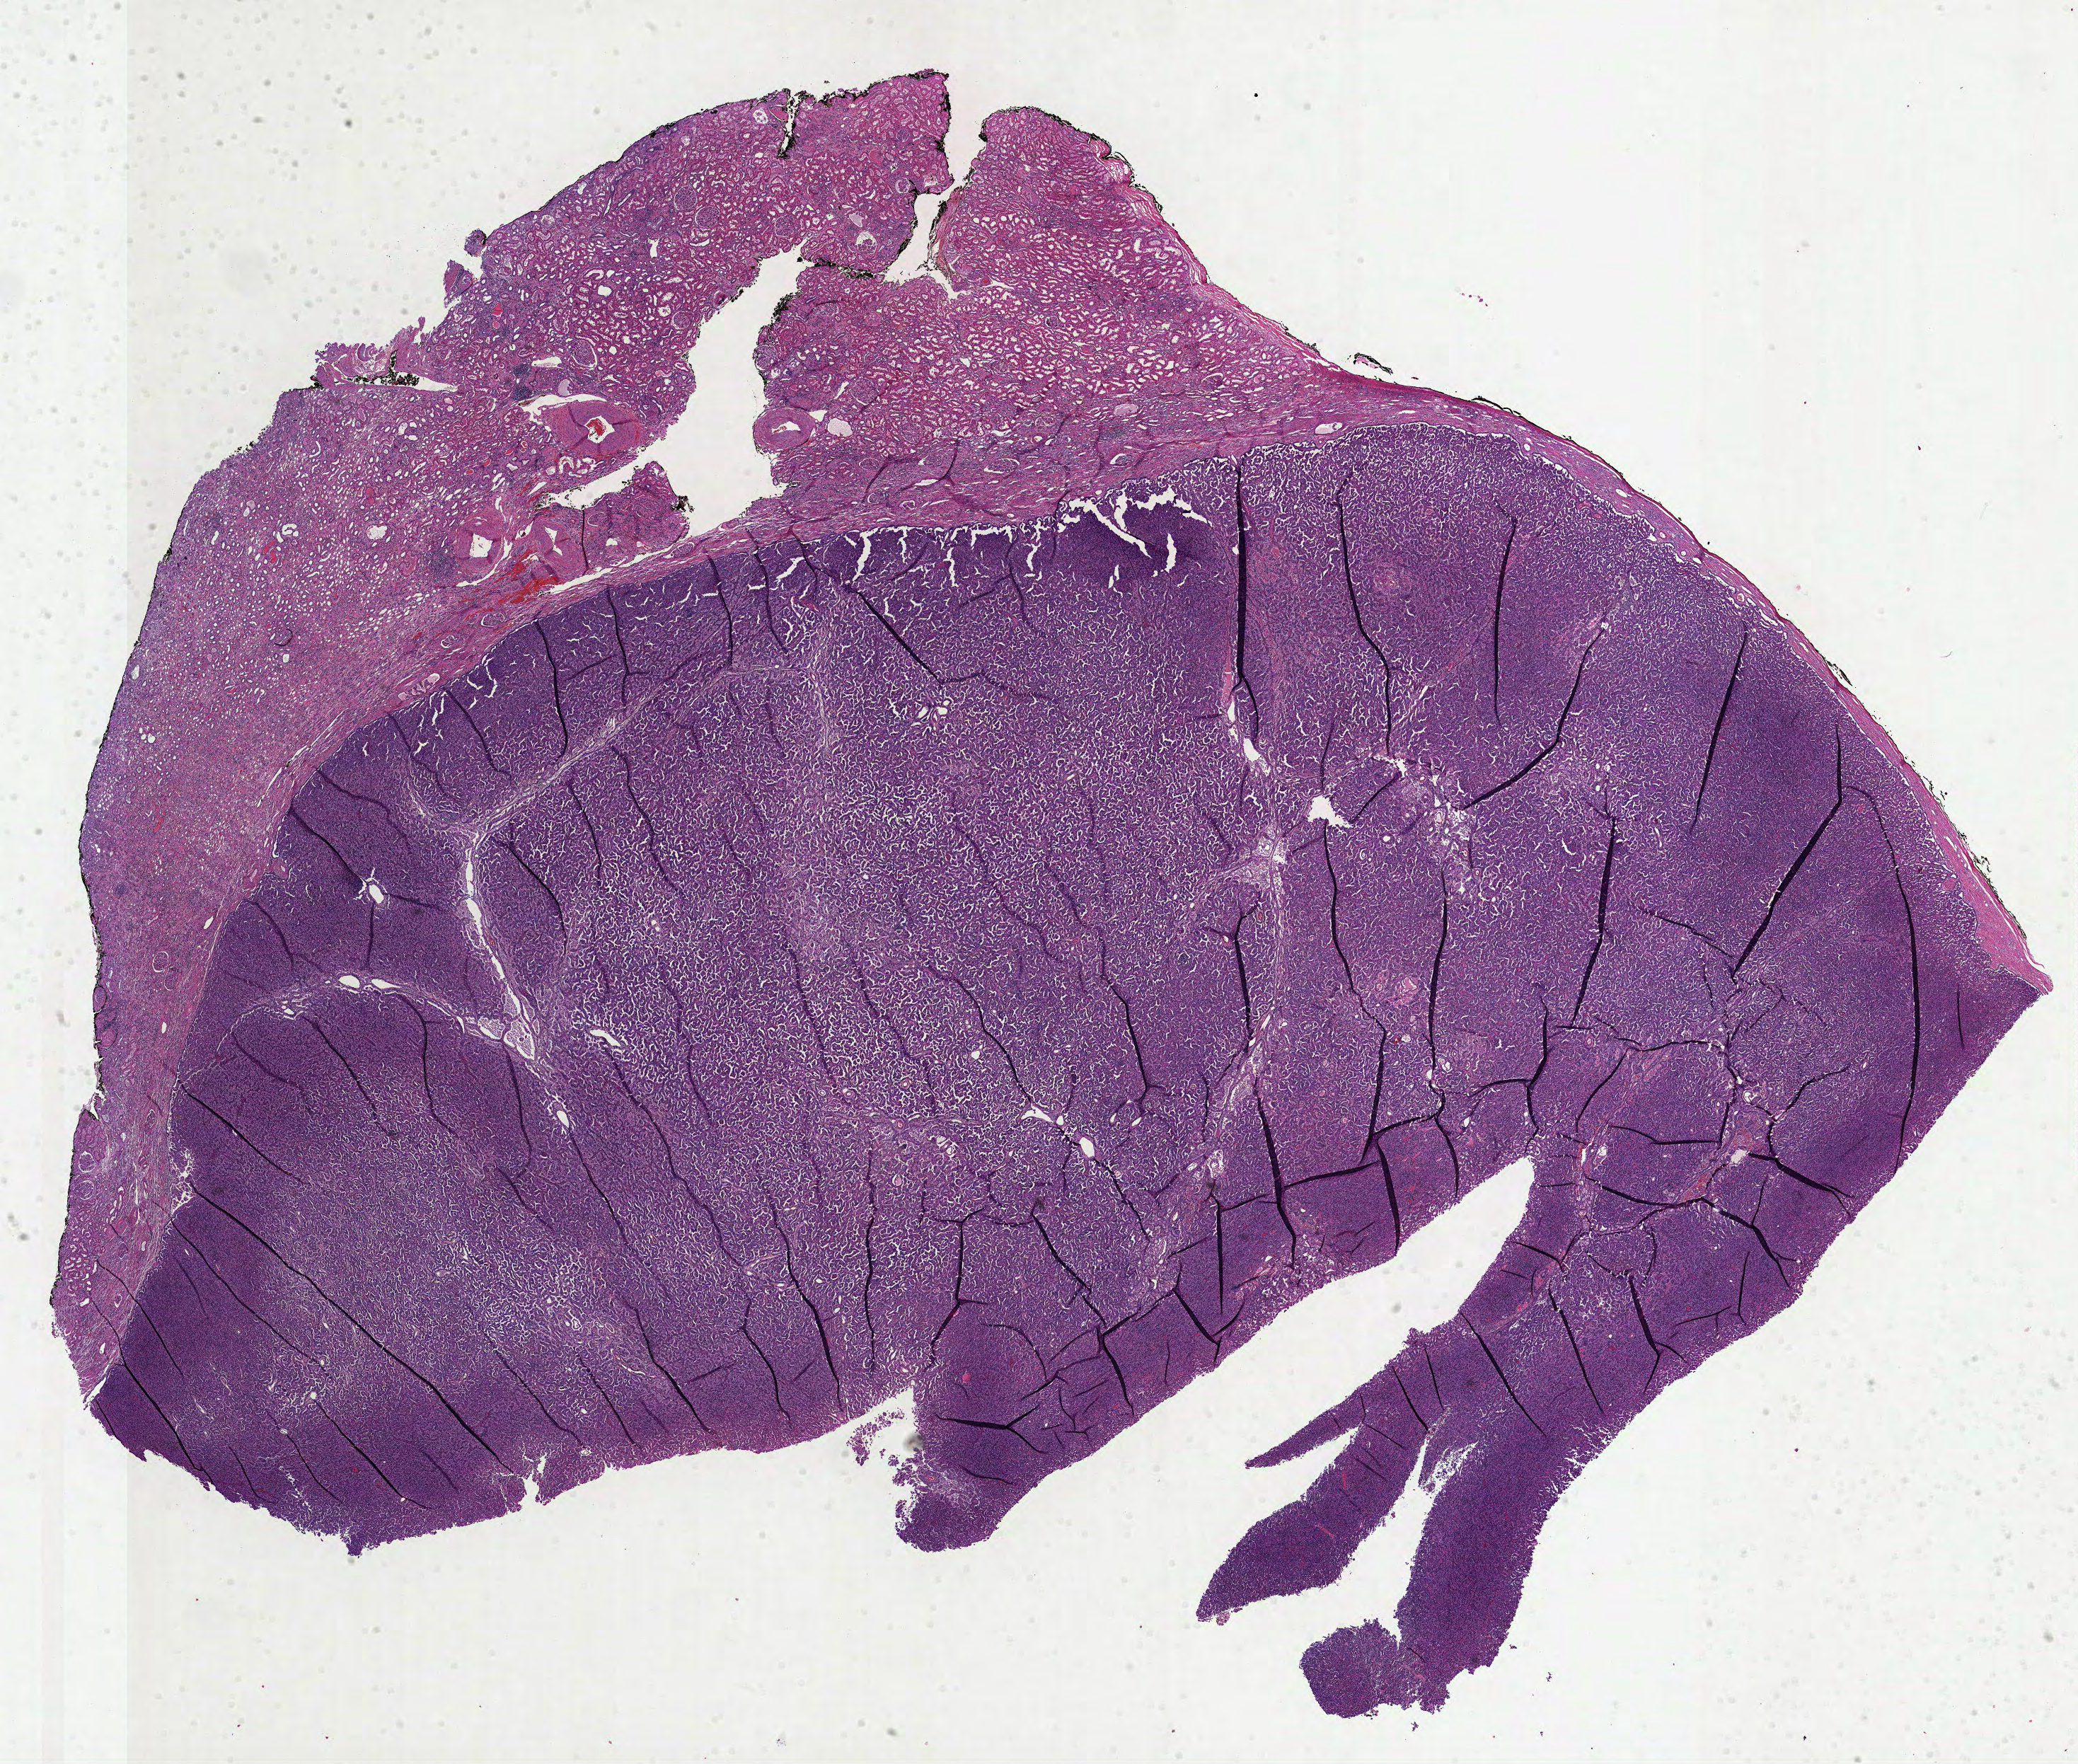
Whole-slide histology image, H&E, shown as a low-resolution overview of the whole scanned area (about 23.7 x 20.1 mm, slide scanned at 40x); formalin-fixed paraffin-embedded (FFPE) diagnostic section; kidney, primary tumour sample. Male patient; age at initial diagnosis 51 years.
Laterality: left. AJCC pathologic stage: I. Histologic diagnosis: Papillary adenocarcinoma, NOS.